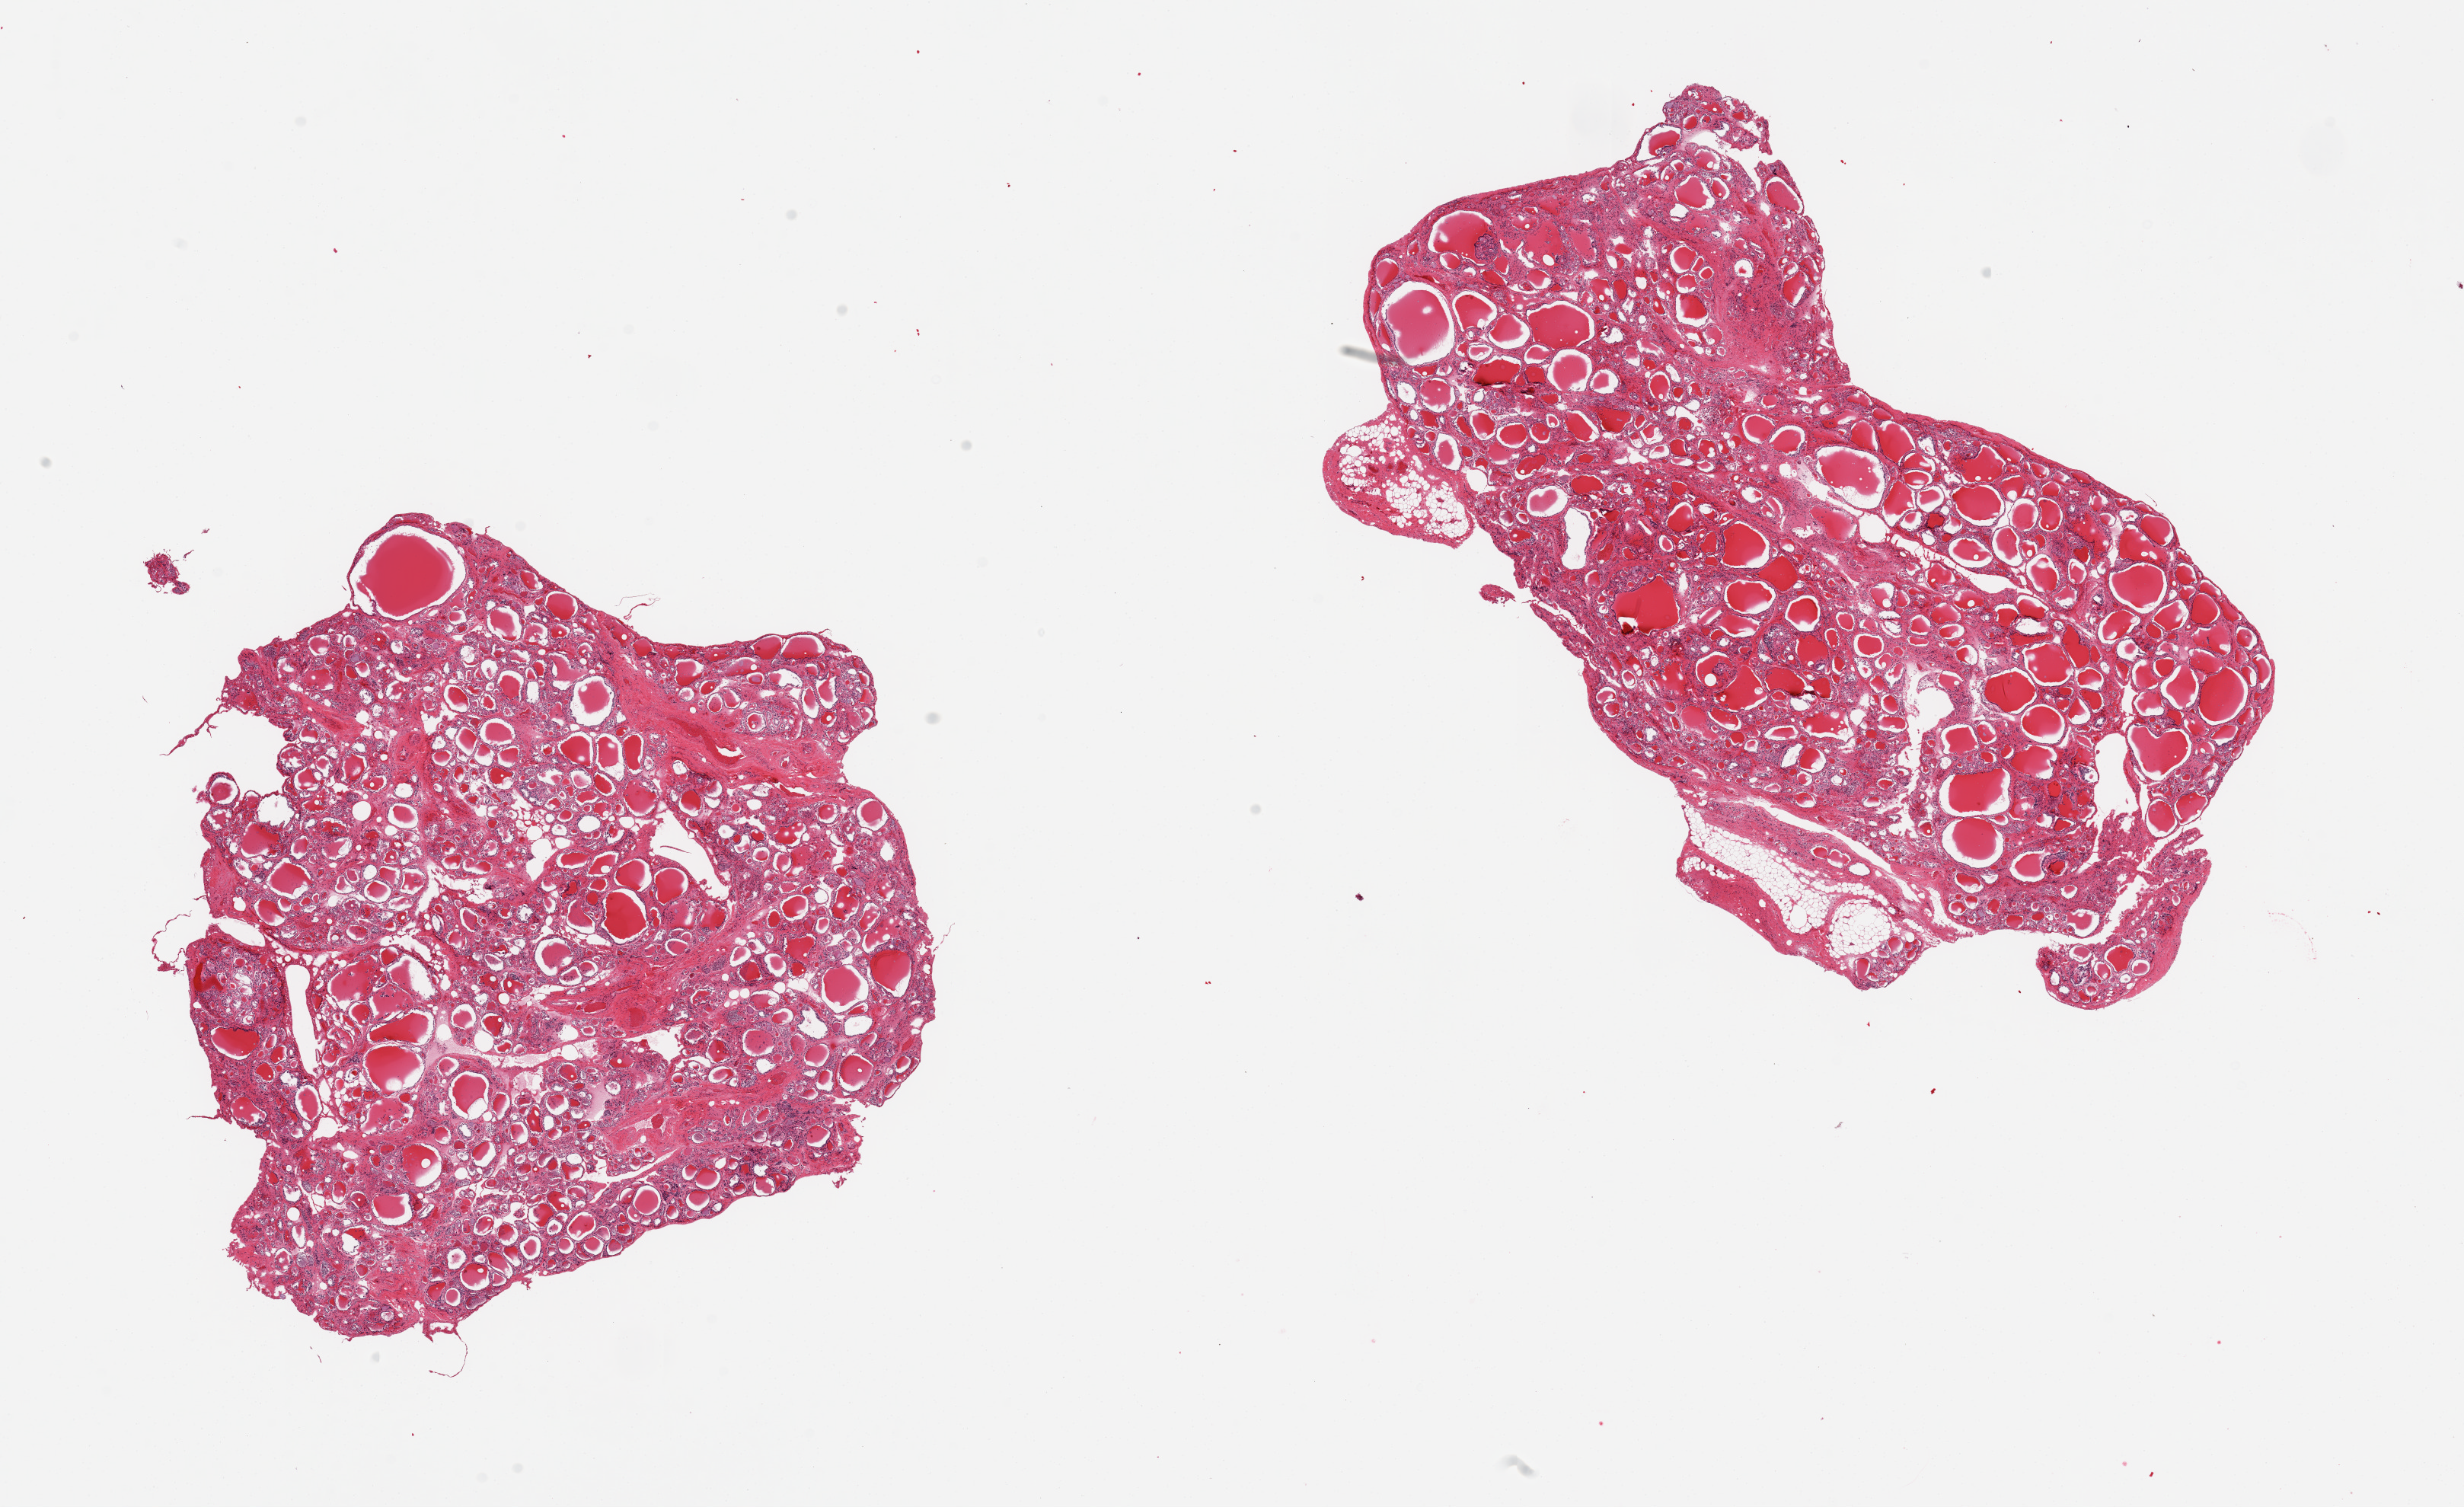
H&E whole-slide image — shown as a low-resolution overview of the whole scanned area (about 25.6 x 15.7 mm, from a 20x scan); PAXgene-fixed, paraffin-embedded tissue; section of thyroid (target tissue); tissue donor sample. Donor sex: male.
Reviewer comment on this tissue sample: 2 pieces; patchy interstitial fibrosis and variably sized follicles; small amount of external fat attached to one piece.